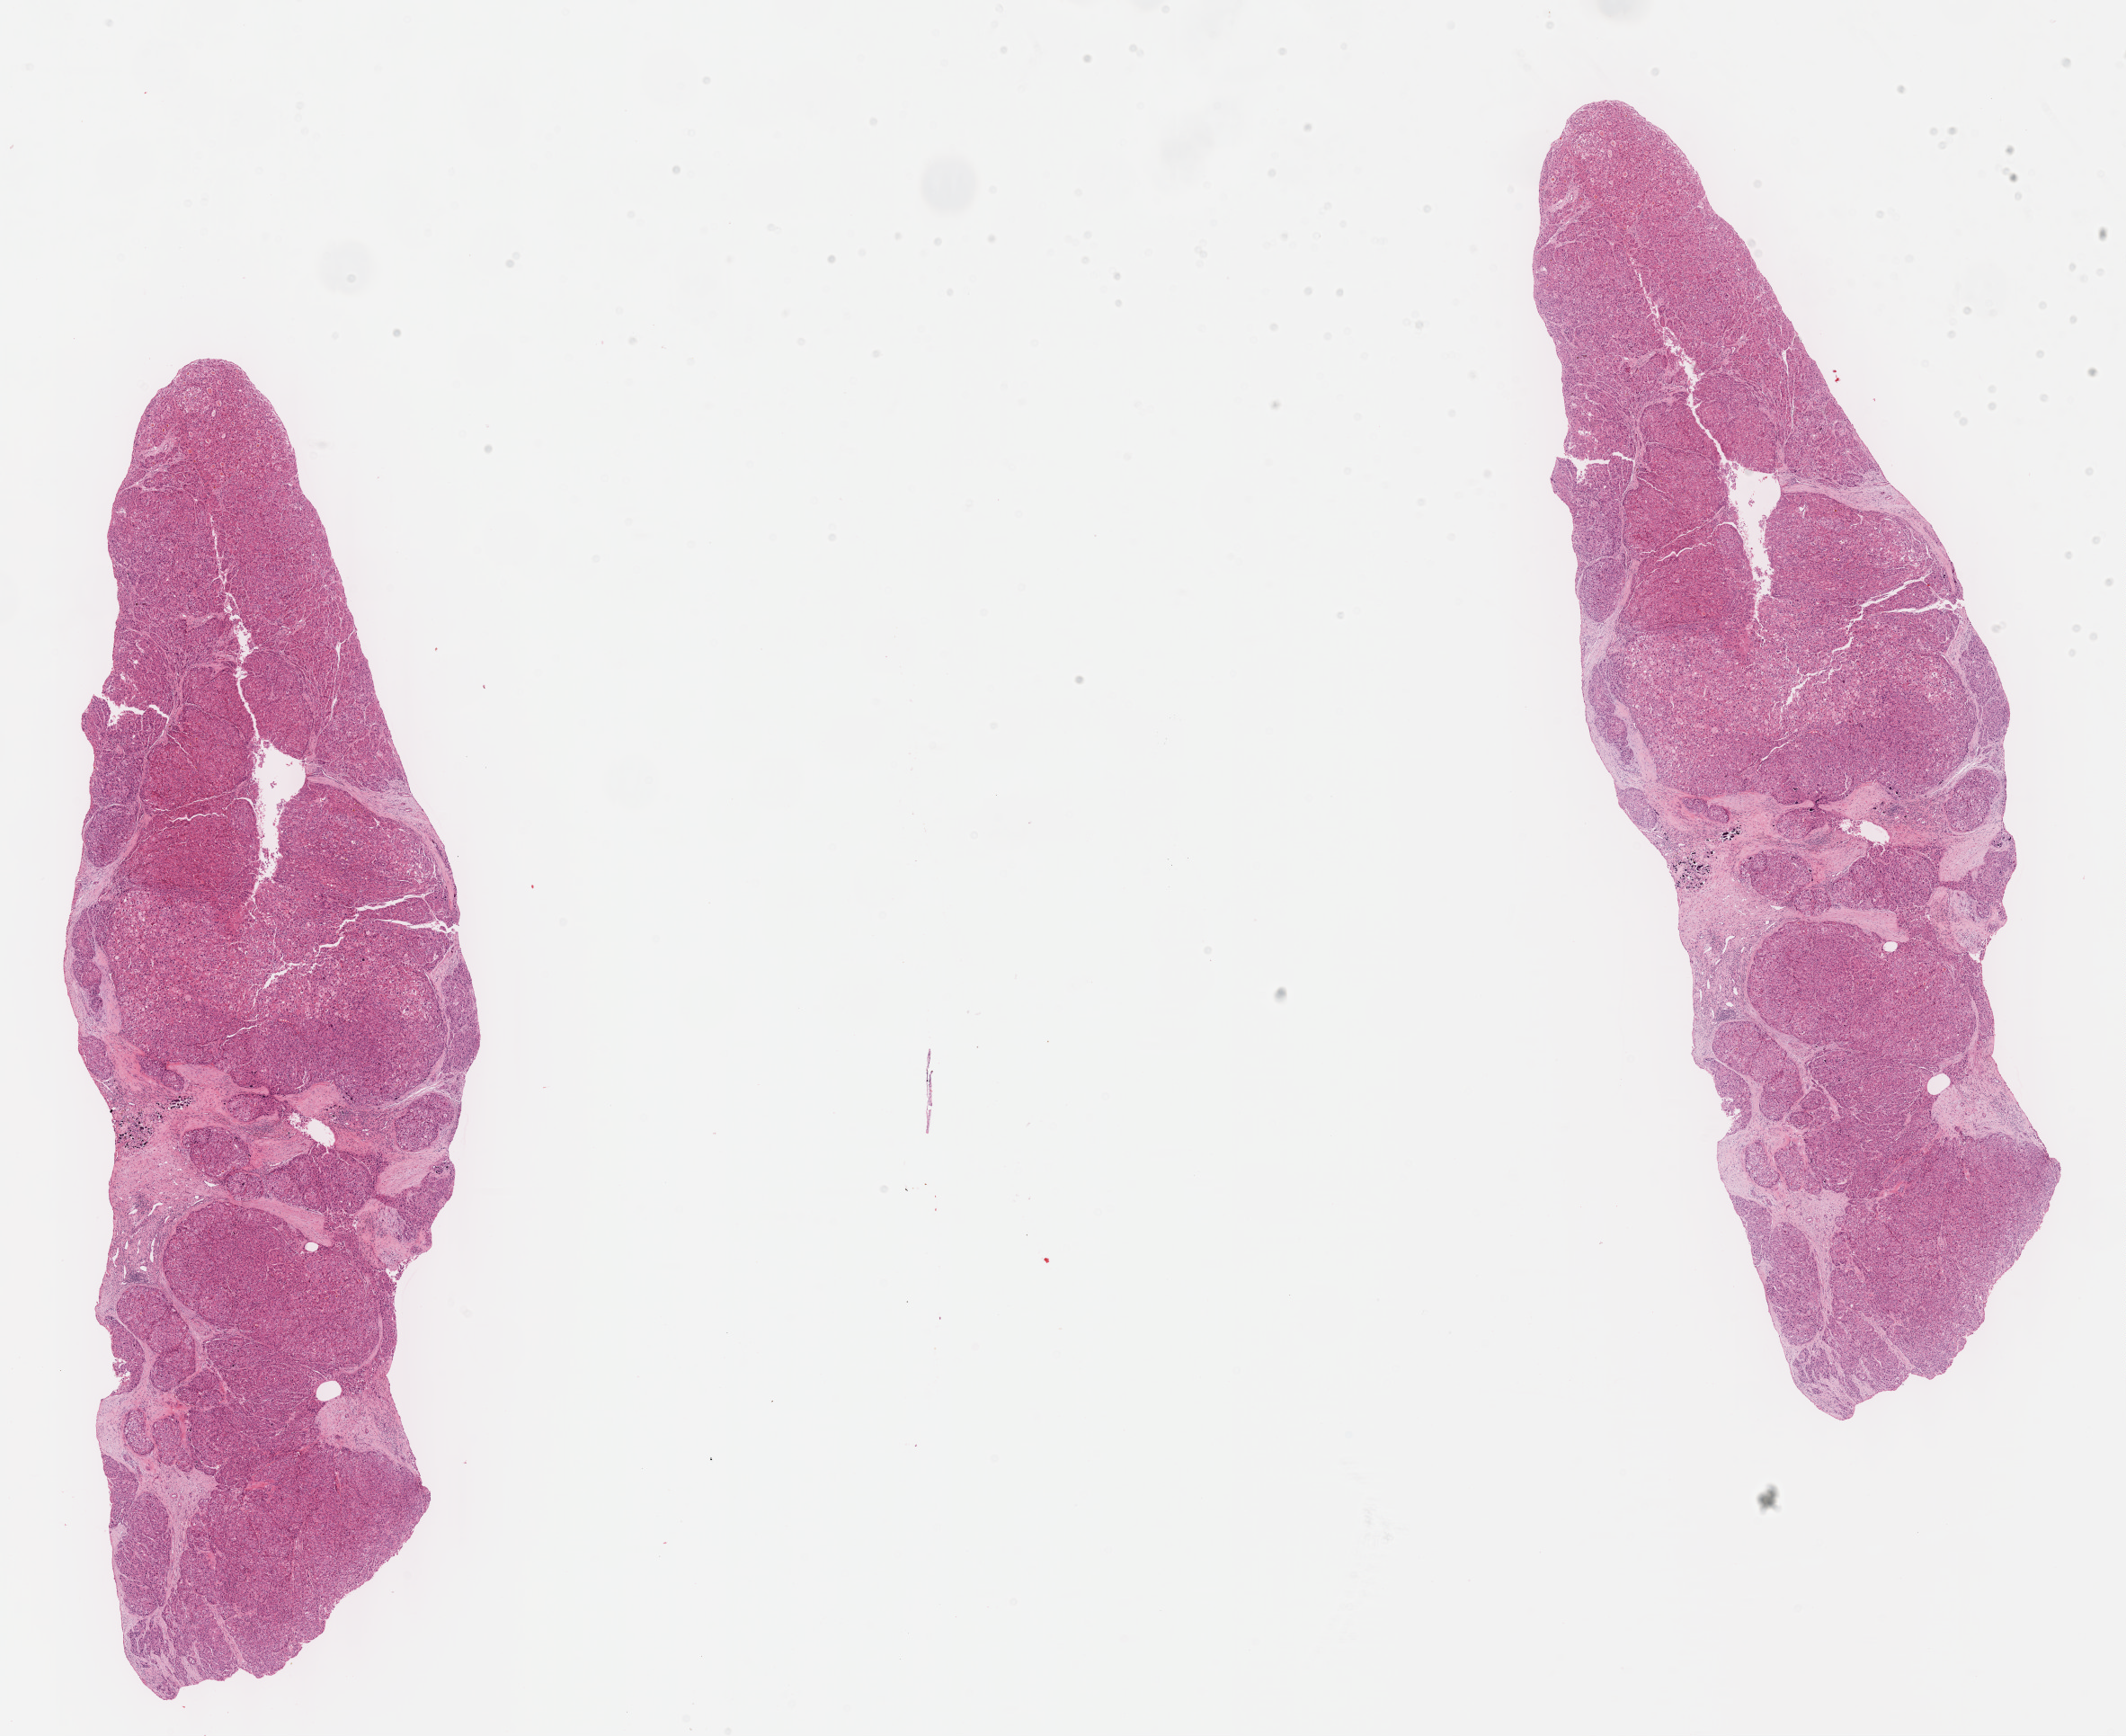
Whole-slide histology image, H&E-stained, a low-resolution overview of the entire scanned area, about 19.1 x 15.6 mm (from a 40x scan). FFPE section. Primary tumour sample from the liver. Female patient; age at initial diagnosis 59 years. Histologic grade: G3 (poorly differentiated).
AJCC pathologic stage: I (7th edition). Diagnosis: Hepatocellular carcinoma, NOS.